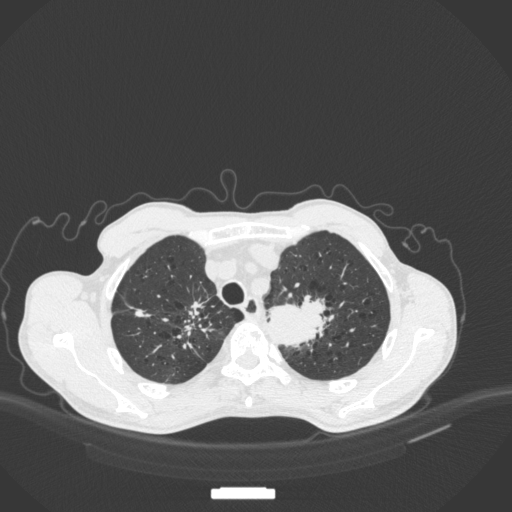
Chest CT, one axial slice. Position 351 of 394 along the scan axis. Reconstruction kernel B31f. 120 kVp. Lung window (W 1500 / L -600 HU). 512 × 512 image matrix, field of view 400 × 400 mm. Patient: male, 65 years. From the clinical record (not read from this slice): clinical TNM (as recorded): T2b N0 M0; histopathological grade: G2.
Outlined on this slice (rectangle marked by the reading radiologist):
- lung tumour (recorded histology: adenocarcinoma): bounding box (x1, y1, x2, y2) in pixels: (262, 287, 334, 350)